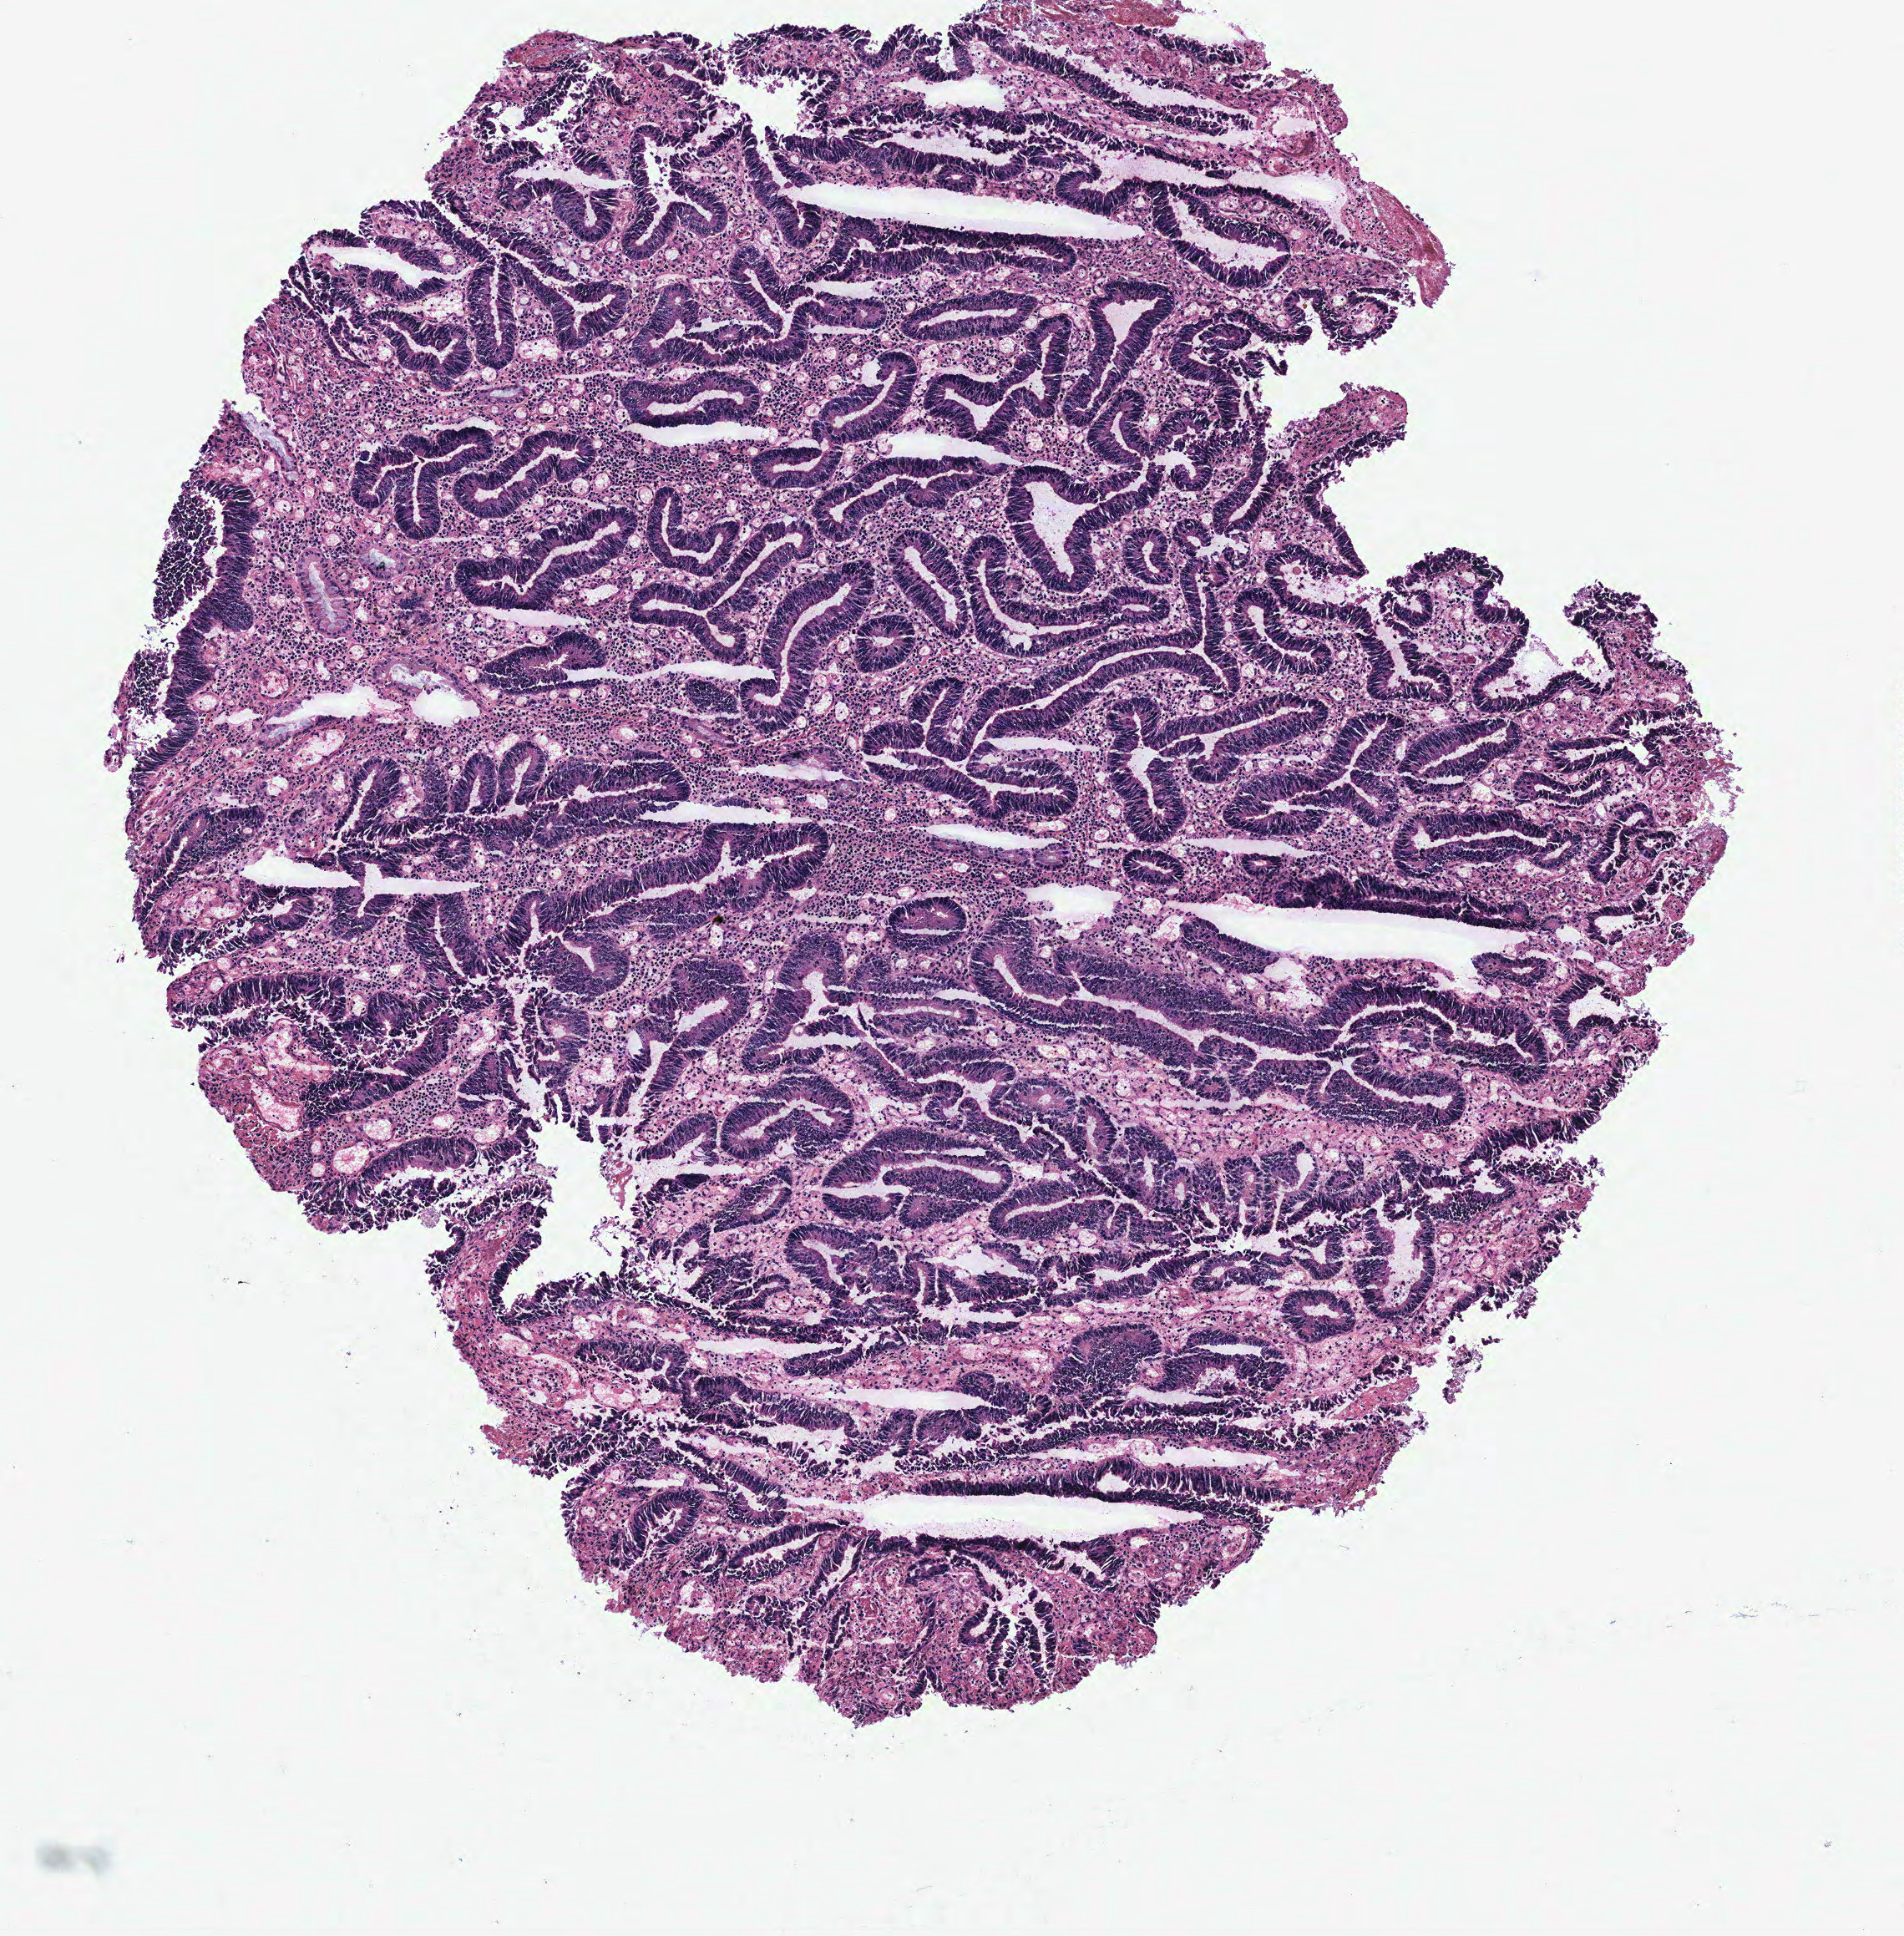
H&E-stained whole-slide image, whole scanned area (about 4.6 x 4.6 mm, acquisition: 40x scan) shown as a low-resolution overview; colon, normal (non-tumour) tissue. Patient: female, age 70 years.
This section: normal (non-tumour) tissue from the same patient. Patient diagnosis: Adenocarcinoma, NOS.